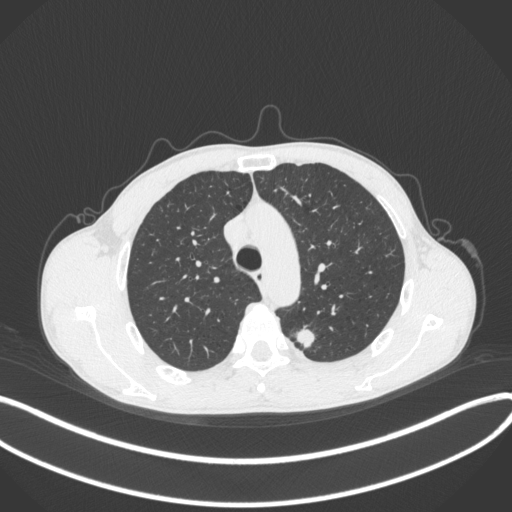
Chest CT, one axial slice. Slice 296 of 429 in the series (ordered by position). 120 kVp. Lung window (W 1500 / L -600 HU). 512 × 512 image matrix, field of view 400 × 400 mm. Patient: male, 51 years. Case-level facts recorded for this patient, not image findings: clinical TNM (as recorded): T2a N1 M1.
Structures marked on this image (bounding box drawn by a radiologist):
- lung tumour (recorded histology: adenocarcinoma): bounding box (x1, y1, x2, y2) in pixels: (294, 321, 315, 353)